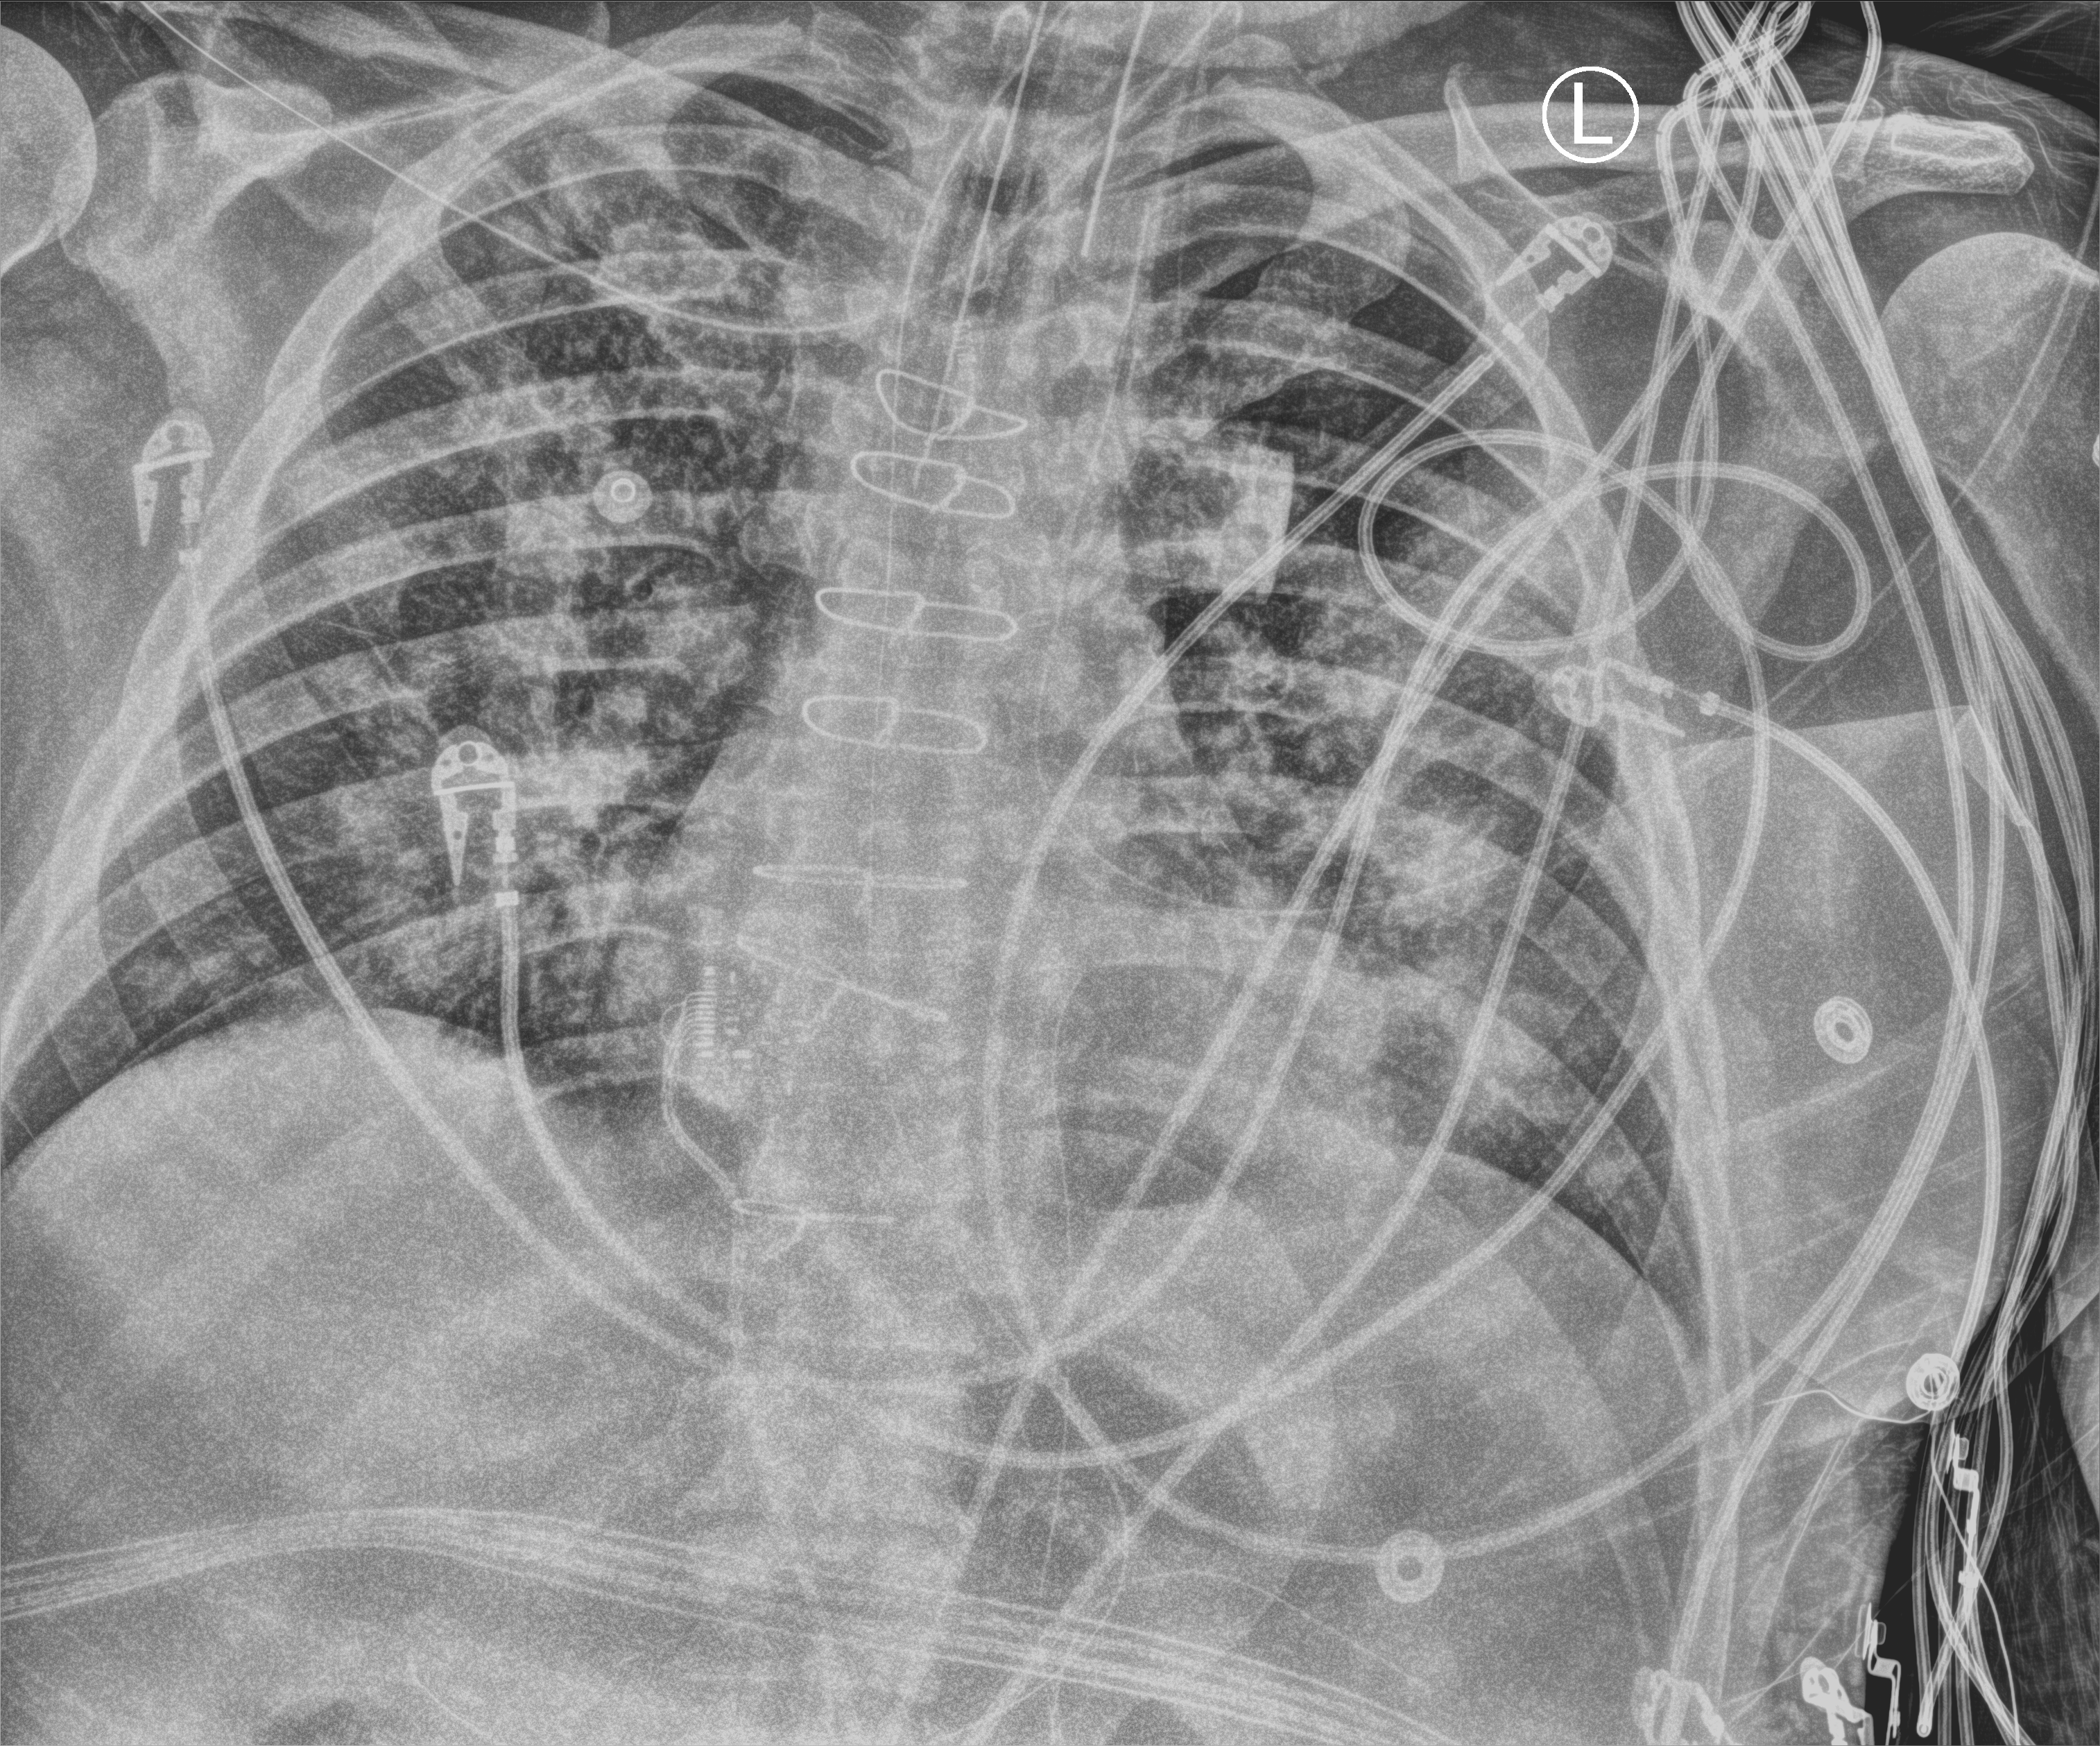
Bedside chest radiograph (computed radiography); anteroposterior (AP) projection. Male patient hospitalised with COVID-19, age 60–74 years.
From the hospital-stay record, not from the radiograph (when in the stay this image was taken is not recorded): mechanically ventilated during this hospital stay: yes; chronic kidney disease (admission record): no.